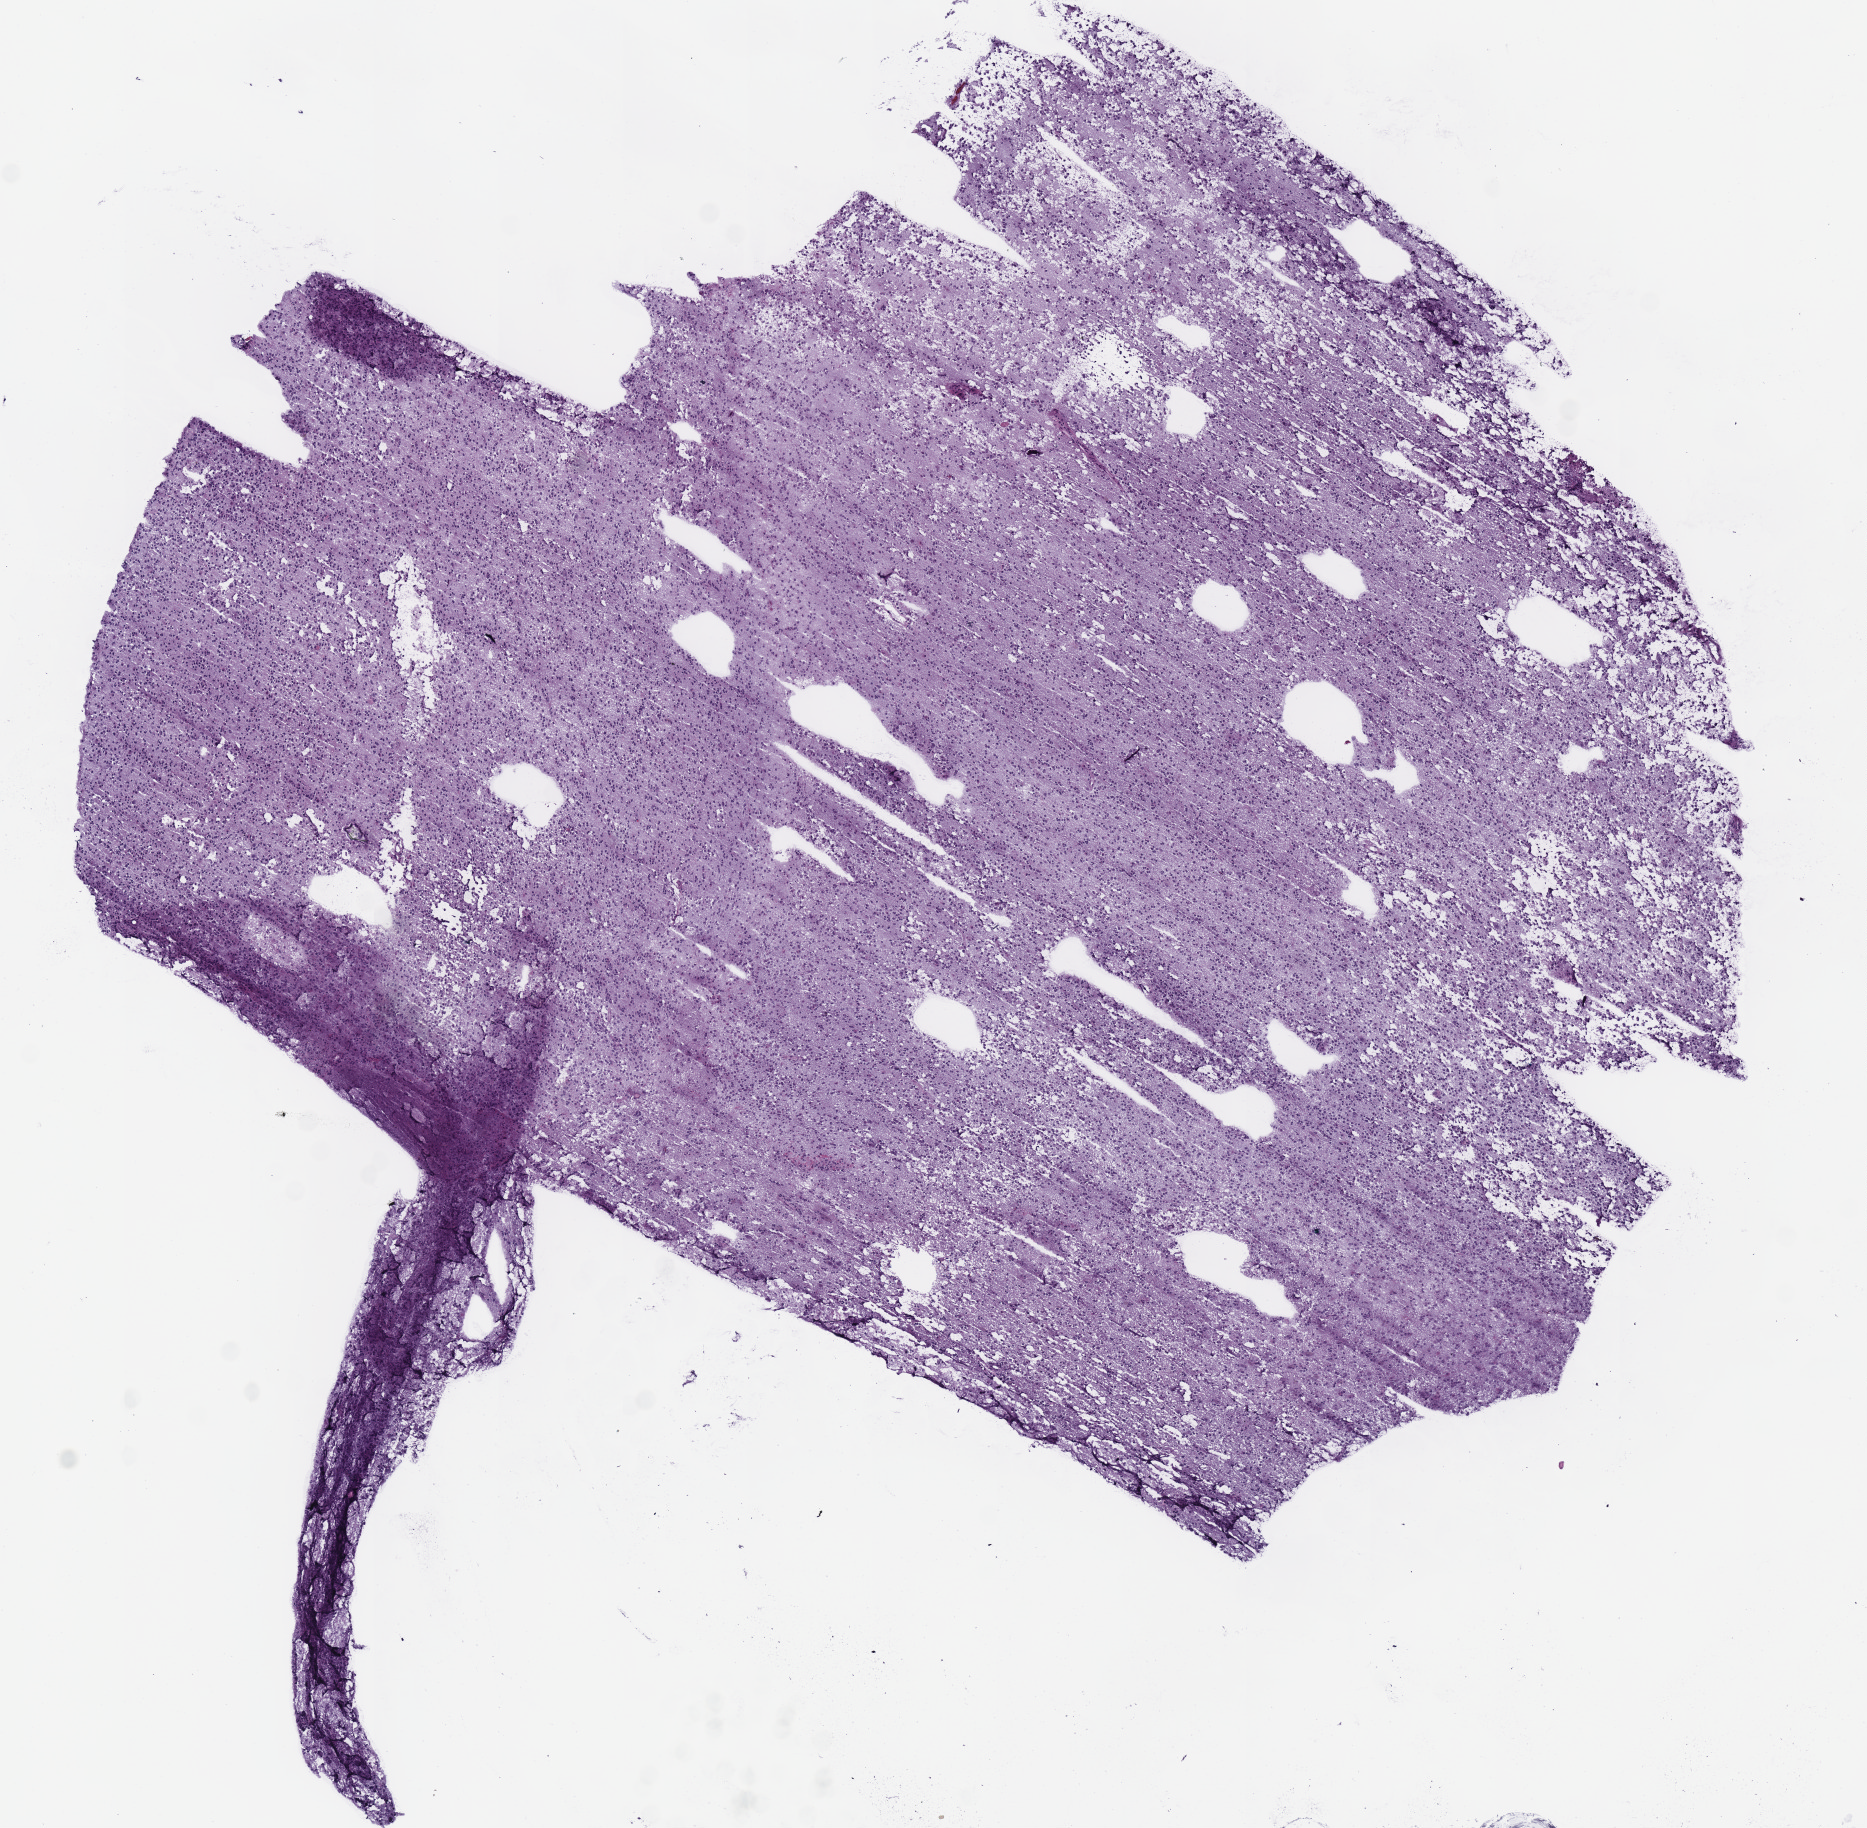
Digitized H&E tissue section (whole slide), low-resolution overview of the scanned area, about 7.3 x 7.2 mm (acquisition: 40x scan), frozen section from the top of the tissue portion, sample: primary tumour, brain. Male patient; age at initial diagnosis 51 years. Histologic grade: G2 (moderately differentiated). Slide review estimates, as recorded: tumour cells 100%, tumour nuclei 80%, normal cells 0%, stromal cells 0%, necrosis 0%.
- laterality: right
- histologic diagnosis: Oligodendroglioma, NOS (cerebrum)